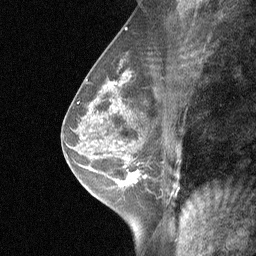
Breast MRI (dynamic contrast-enhanced), one sagittal slice. Slice 35 of 64 in the series (ordered by position). Dynamic contrast-enhanced study with each time point stored as its own series, time point 2 of 3 at this slice position (early post-contrast, ordered by acquisition time). 1.5 T. TE 4.8 ms, TR 27 ms. 256 × 256 image matrix, field of view 180 × 180 mm. Patient: female, 47 years. From the clinical record (not read from this slice): setting: breast cancer imaged before/during neoadjuvant chemotherapy; receptor status: HR-positive, HER2-negative.
Annotated regions visible in this slice (semi-automatically segmented with operator editing):
- analysis volume of interest (the breast-tissue region the enhancement analysis was run in; not a lesion): box from (x=104, y=138) to (x=165, y=198) px
- tumour enhancement mask (voxels above the 90 % enhancement threshold inside the analysis volume of interest): (x=119, y=148)–(x=139, y=186)